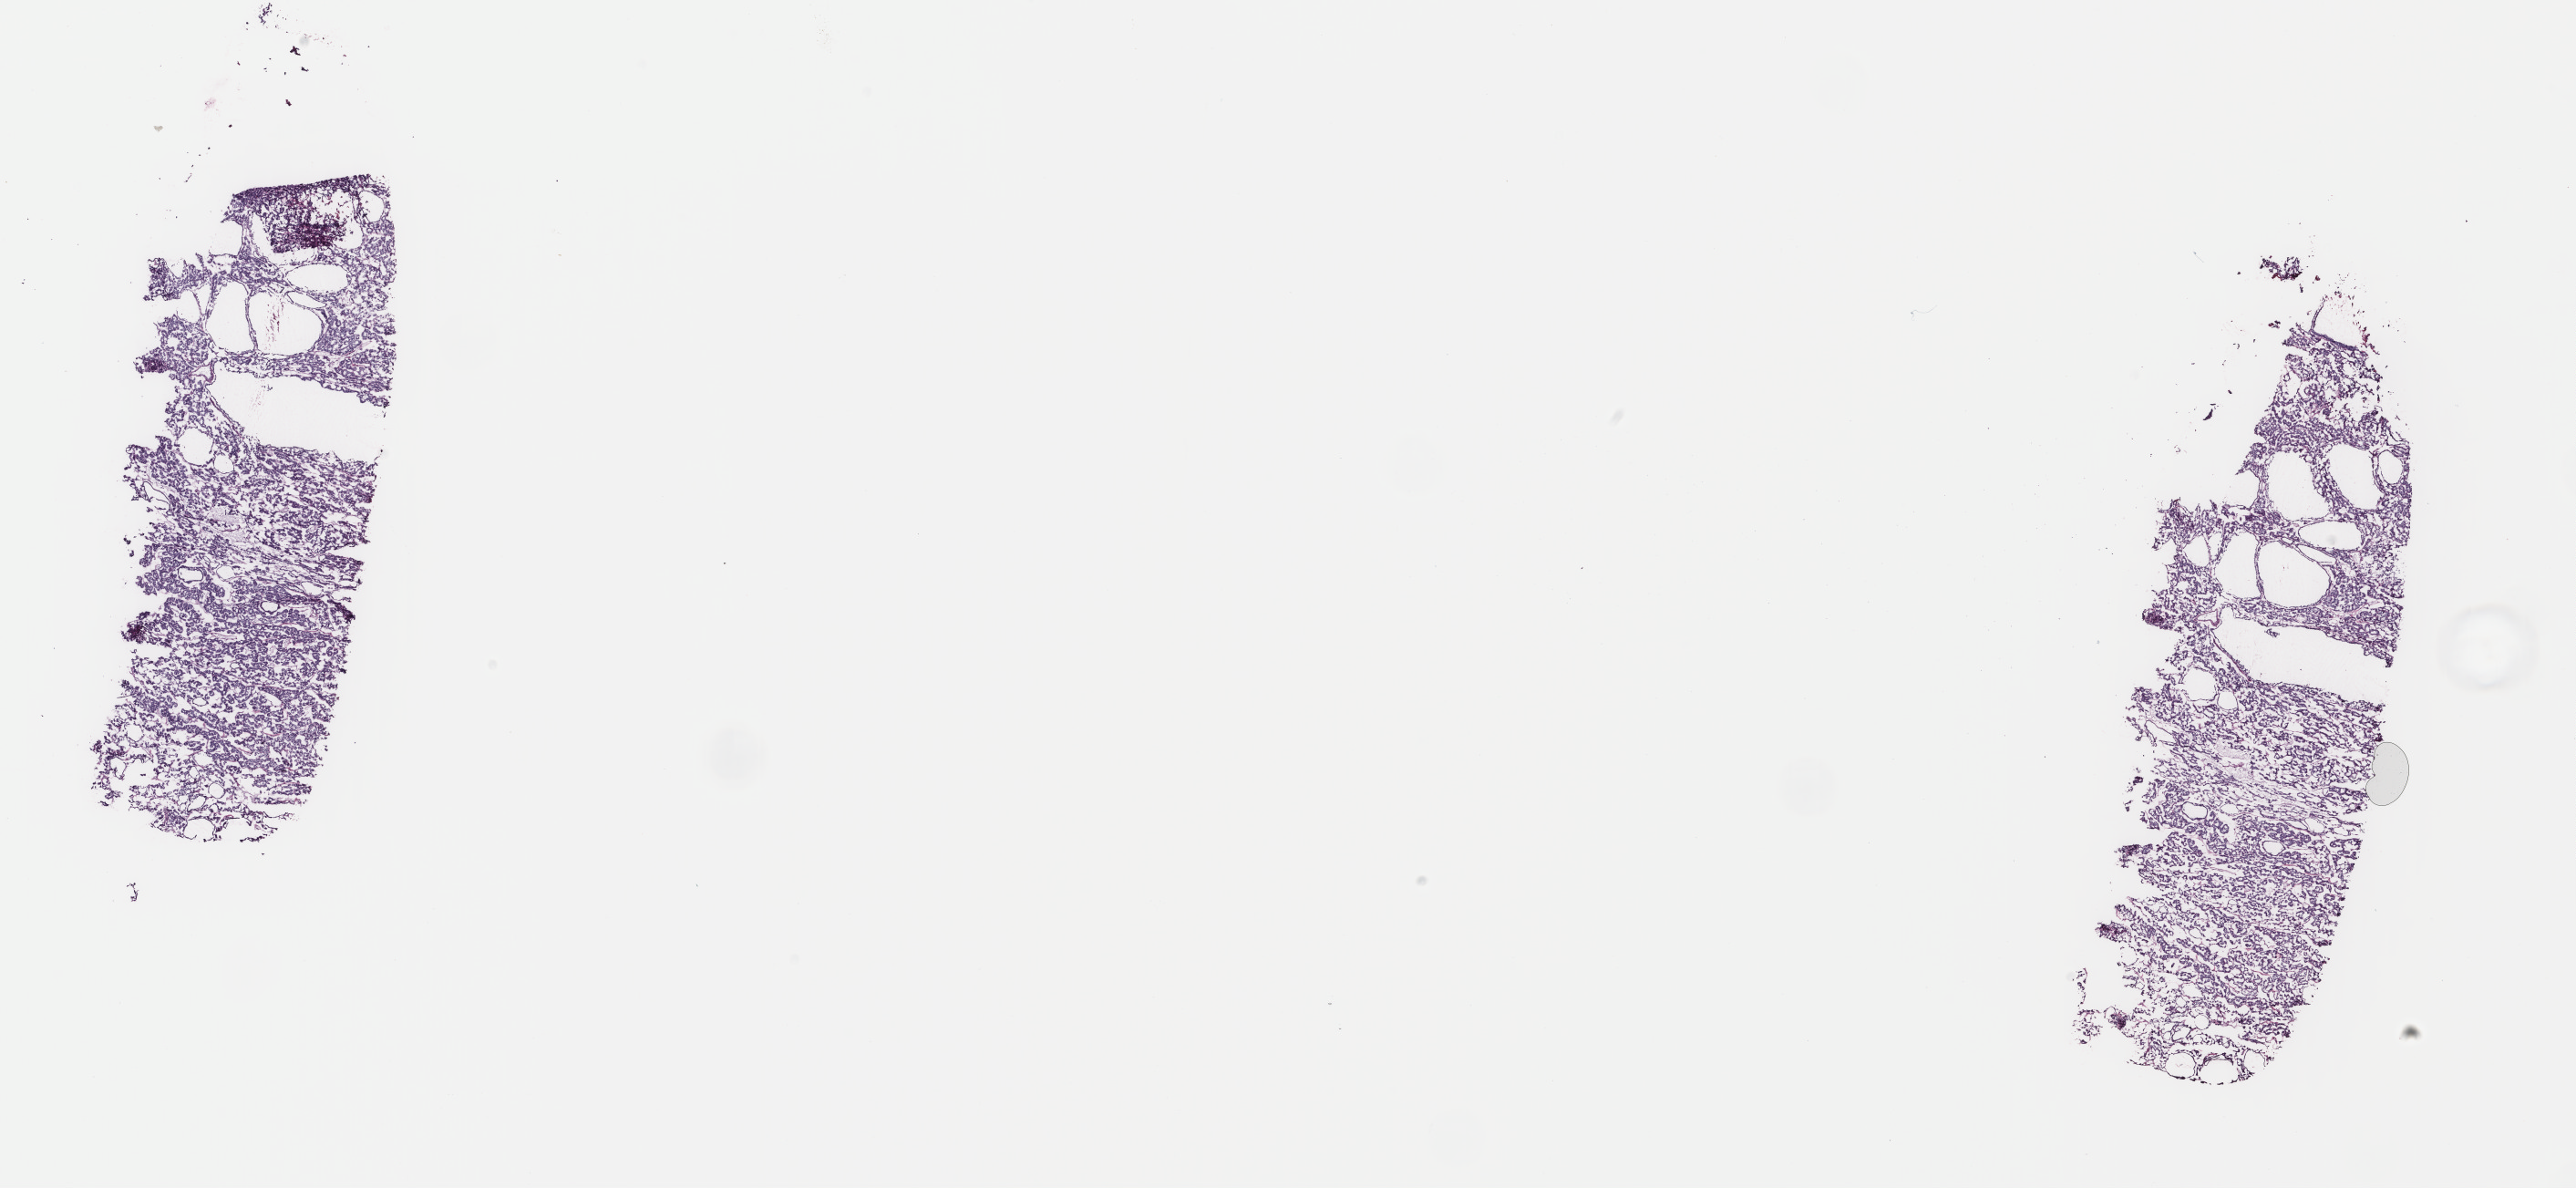
Whole-slide histology image, H&E, a low-resolution overview of the entire scanned area, about 22.4 x 10.3 mm, frozen section from the top of the tissue portion, sample: primary tumour, thyroid. Patient: female, age at initial diagnosis 61 years.
Diagnosis: Papillary adenocarcinoma, NOS (thyroid gland).